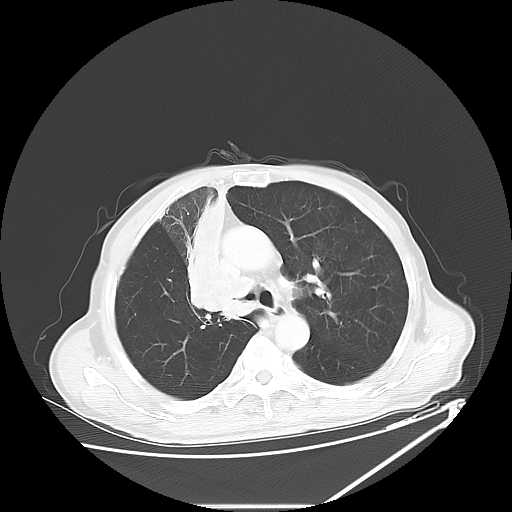
Chest CT, one axial slice. 120 kVp. Lung window (W 1500 / L -600 HU). 5 mm slice thickness. 512 × 512 image matrix, field of view 410 × 410 mm. Male patient, age 73 years. From the clinical record (not read from this slice): clinical TNM (as recorded): T2a N1 M0.
Annotated regions visible in this slice (rectangle marked by the reading radiologist):
- lung tumour (recorded histology: squamous cell carcinoma): bounding box (x1, y1, x2, y2) in pixels: (181, 190, 237, 320)